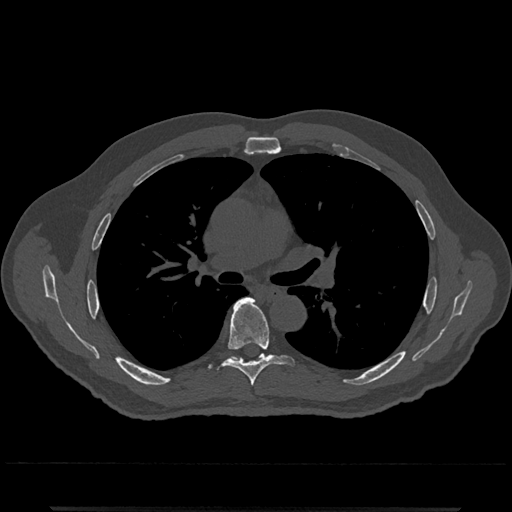
CT including the spine, one axial slice; reconstruction kernel Br40s/3; bone window (W 1800 / L 400 HU); 512 × 512 image matrix, field of view 393 × 393 mm. Patient: male, 67 years. From the clinical record (not read from this slice): primary cancer: prostate.
Outlined on this slice (semi-automatic segmentation, software-assisted and operator-edited):
- T6 vertebra: bounding box [x1, y1, x2, y2] px = [224, 297, 294, 386]